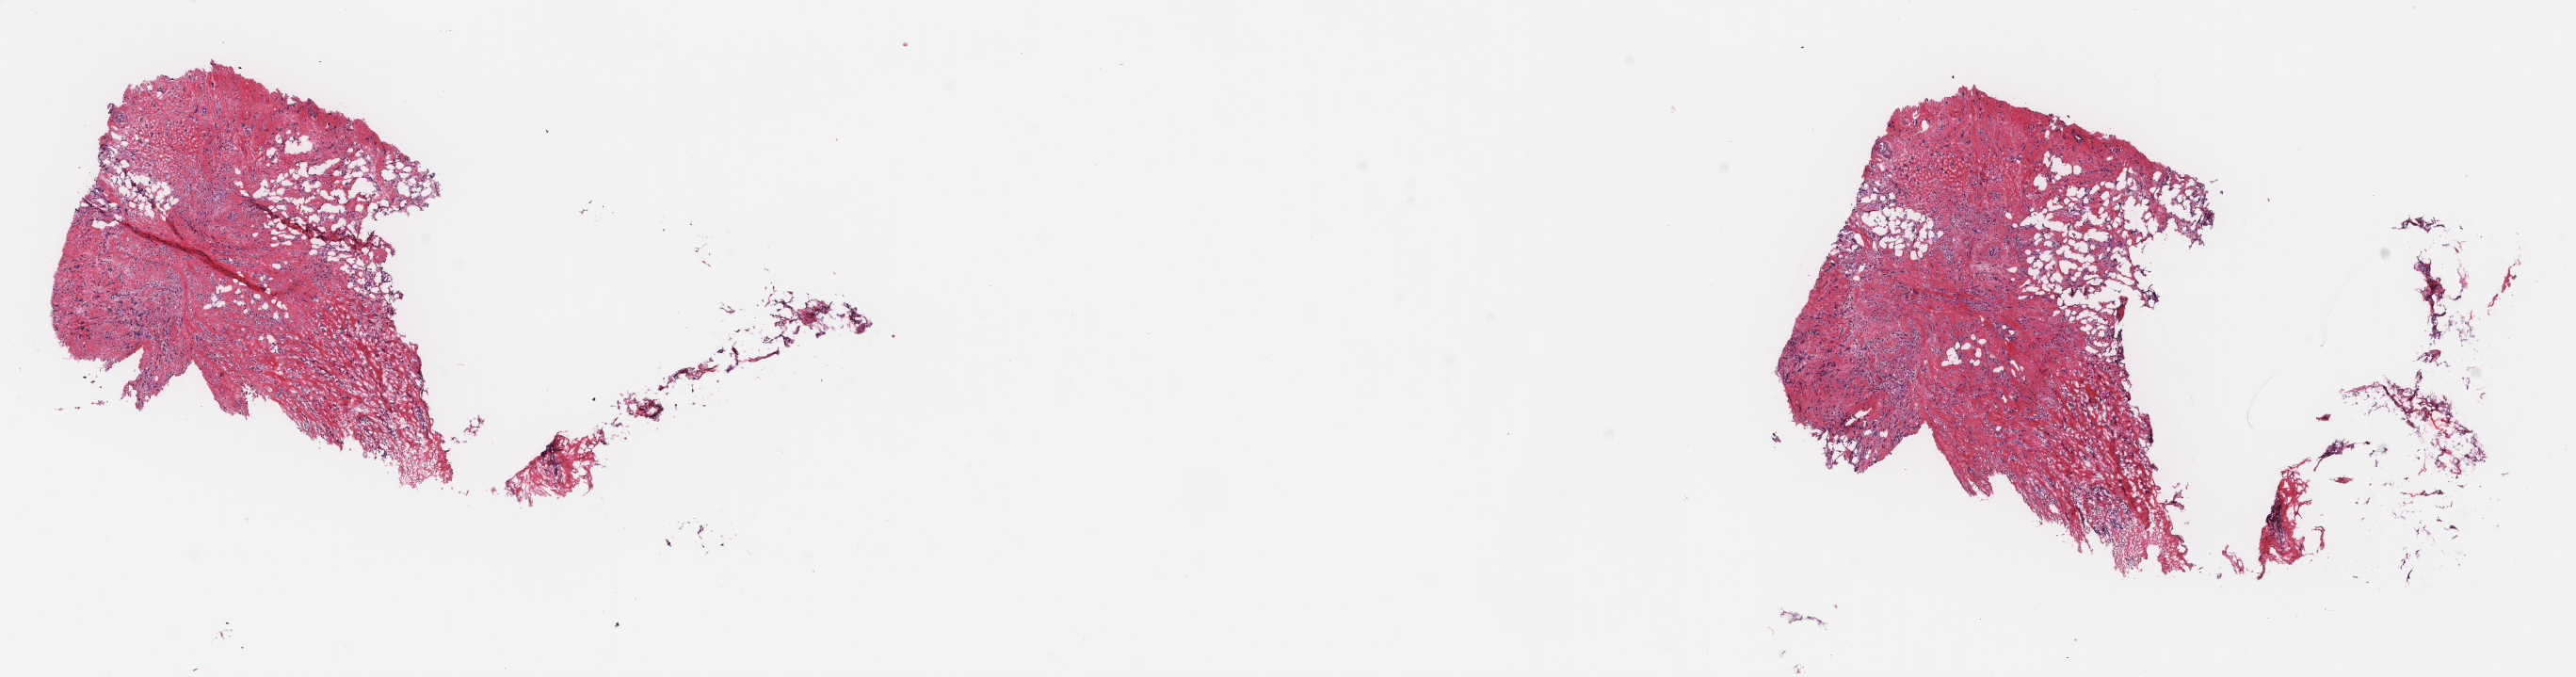
Digitized H&E-stained tissue section (whole slide), shown as a low-resolution overview of the whole scanned area (about 21.7 x 5.7 mm), frozen section, primary tumour sample from the breast. Female, age 65 years at initial diagnosis. Pathologist review of this section (percent, as recorded): tumour cells 40%, tumour nuclei 75%, normal cells 1%, stromal cells 59%, necrosis 0%. Inflammatory infiltration, as recorded: lymphocyte infiltration 1%, monocyte infiltration 0%, neutrophil infiltration 0%.
Histologic diagnosis: Lobular carcinoma, NOS. Laterality: right. Lymph nodes positive (case pathology): 0 of 2 examined. AJCC pathologic stage: IIA (7th edition).